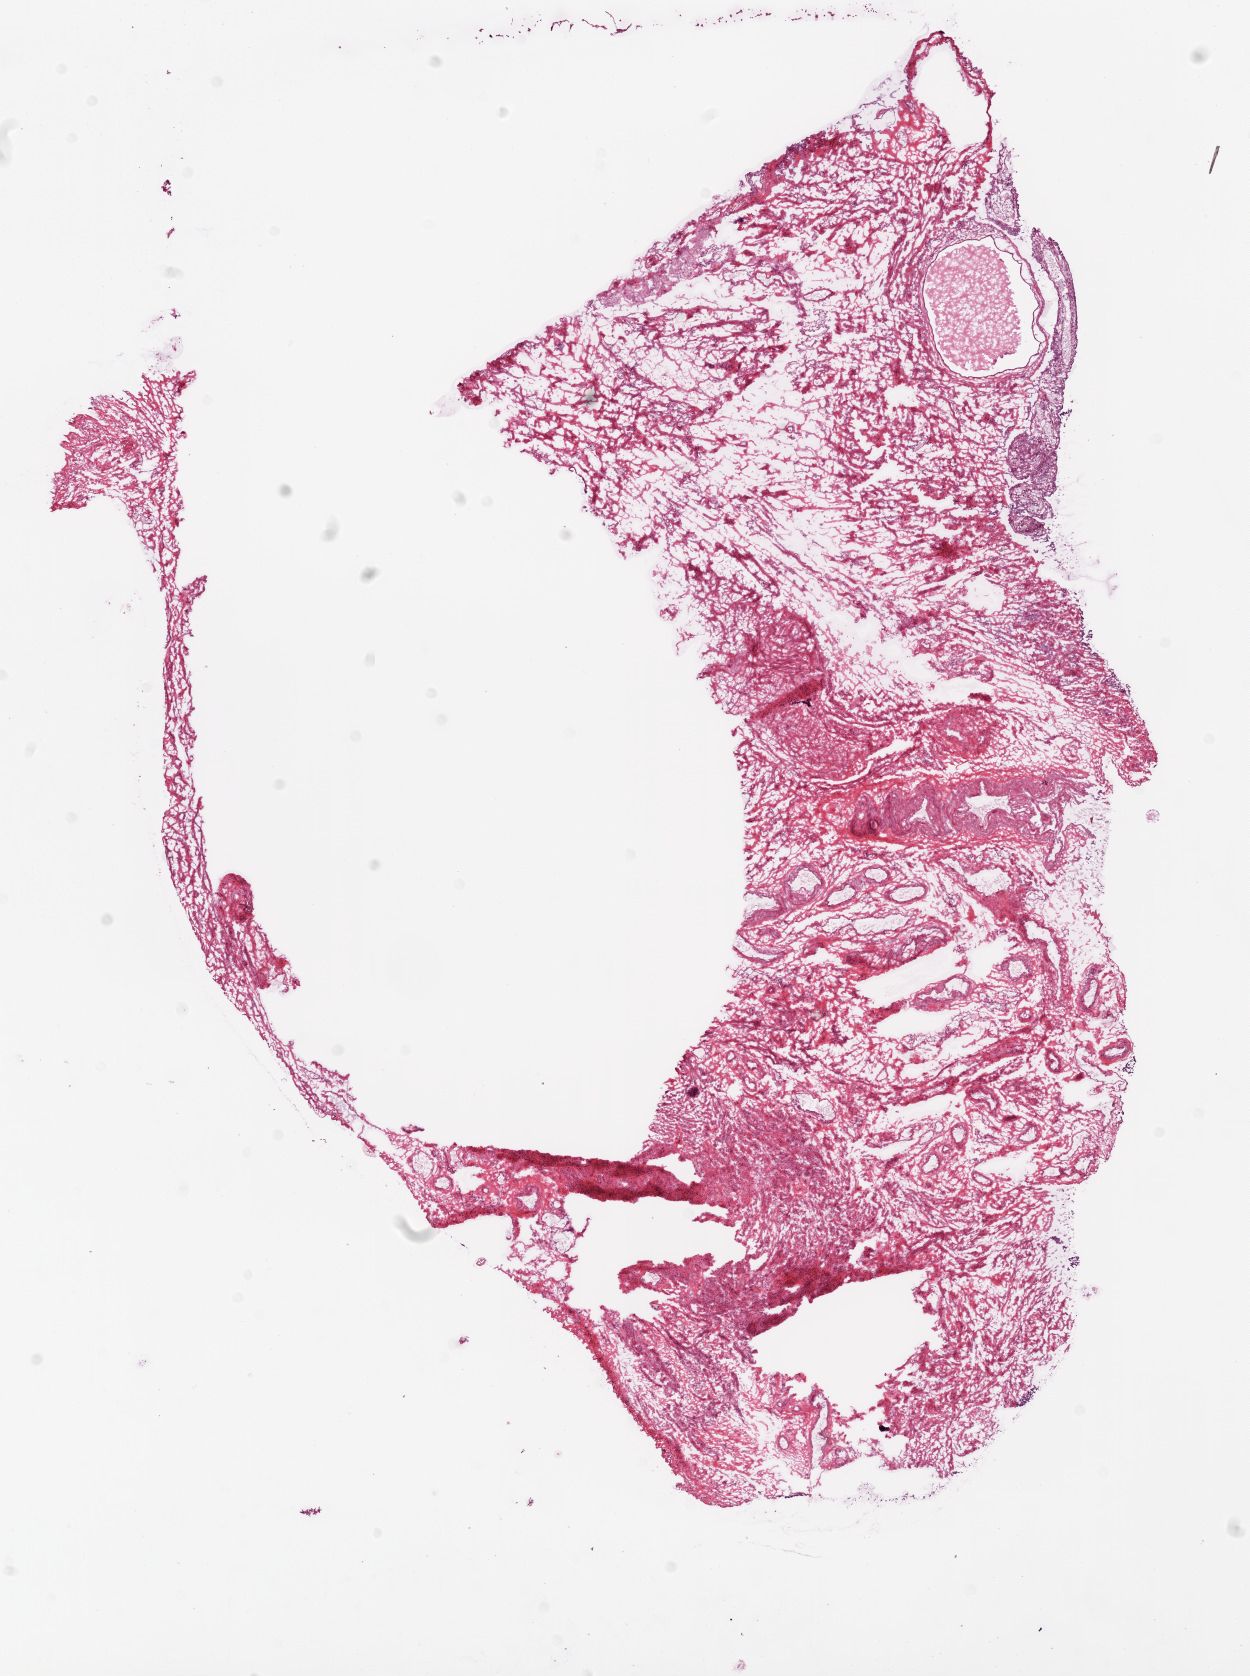
Whole-slide histology image, Hematoxylin and eosin (H&E) stained — low-resolution overview of the scanned area, about 10.0 x 13.4 mm (slide scanned at 20x), frozen section from the bottom of the tissue portion, solid tissue normal (non-tumour tissue) sample from the ovary. Female, age 67 years at initial diagnosis.
- this section: solid tissue normal (non-tumour) sample from the same patient
- patient diagnosis: Serous cystadenocarcinoma, NOS